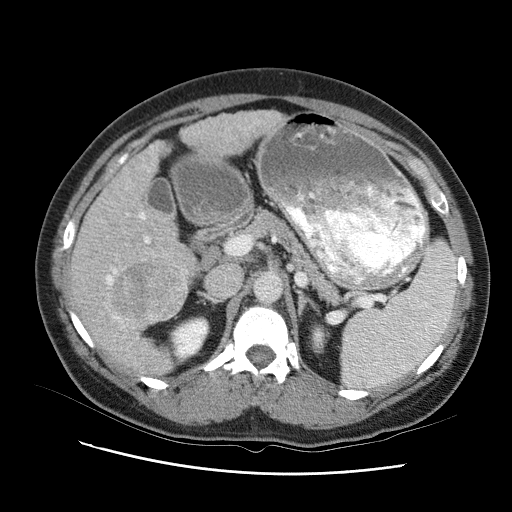
Contrast-enhanced abdominal CT (liver protocol), one axial slice; position 52 of 95 along the scan axis; reconstruction kernel STANDARD; 120 kVp; one of 2 acquisitions stored at this slice position; soft-tissue window (W 400 / L 40 HU); 2.5 mm slice thickness; 512 × 512 image matrix, field of view 360 × 360 mm. Case-level facts recorded for this patient, not image findings: diagnosis: hepatocellular carcinoma (patient treated with transarterial chemoembolisation; whether this scan precedes or follows treatment is not stated here); TNM stage (as recorded): Stage-I; Child-Pugh class: B; tumour differentiation: moderately differentiated.
Outlined on this slice (semi-automatic segmentation, software-assisted and operator-edited):
- liver parenchyma outside the tumour (the mass and vessels are separate outlines, so this box may not span the whole liver): bounding box (x1, y1, x2, y2) in pixels: (66, 104, 284, 374)
- mass: (125, 254, 192, 319)
- liver vessels: (105, 121, 250, 356)